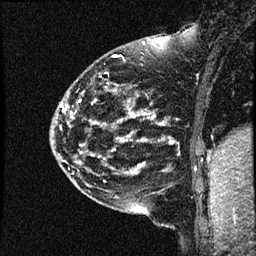
Breast MRI (dynamic contrast-enhanced), one sagittal slice. Position 13 of 44 along the scan axis. Dynamic contrast-enhanced study with each time point stored as its own series, time point 2 of 4 at this slice position (early post-contrast, ordered by acquisition time). 1.5 T. TE 4.2 ms, TR 17.7 ms. 2 mm slice thickness. 256 × 256 image matrix, field of view 200 × 200 mm. Female patient, age 52 years. Case-level facts recorded for this patient, not image findings: setting: breast cancer imaged before/during neoadjuvant chemotherapy; receptor status: HR-positive, HER2-negative.
Outlined on this slice (semi-automatically segmented with operator editing):
- analysis volume of interest (the breast-tissue region the enhancement analysis was run in; not a lesion): bounding box [x1, y1, x2, y2] px = [50, 48, 163, 147]
- tumour enhancement mask (voxels above the 100 % enhancement threshold inside the analysis volume of interest): [81, 116, 156, 146]